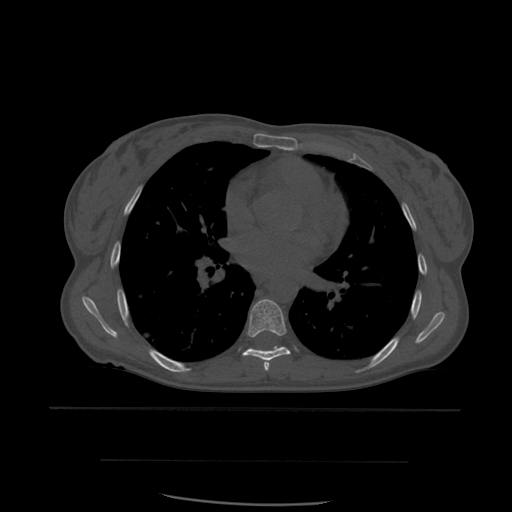
CT including the spine, one axial slice; position 373 of 574 along the scan axis; bone window (W 1800 / L 400 HU); 1.25 mm slice thickness; 512 × 512 image matrix. Patient age 48 years. Case-level facts recorded for this patient, not image findings: primary cancer: lung; vertebrae with lytic lesions (as recorded): T11.
Annotated regions visible in this slice (semi-automatically segmented with operator editing):
- T6 vertebra: box from (x=264, y=362) to (x=269, y=371) px
- T7 vertebra: (x=243, y=299)–(x=291, y=367)
- T8 vertebra: (x=250, y=347)–(x=285, y=350)